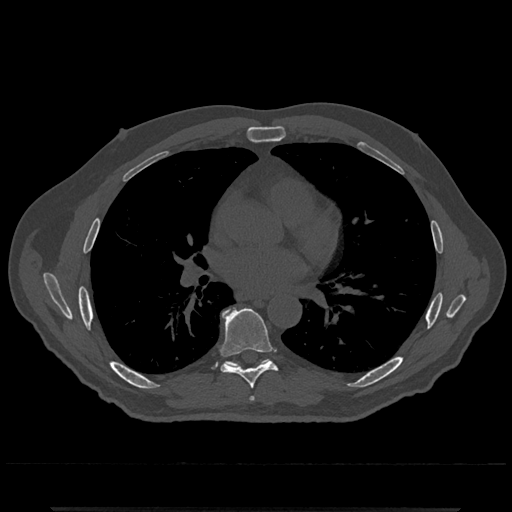
CT including the spine, one axial slice; position 713 of 797 along the scan axis; reconstruction kernel Br40s/3; 120 kVp; bone window (W 1800 / L 400 HU); 512 × 512 image matrix, field of view 393 × 393 mm. Patient: male, 67 years. From the clinical record (not read from this slice): primary cancer: prostate.
Structures marked on this image (semi-automatic segmentation, software-assisted and operator-edited):
- T6 vertebra: bounding box <250,397,254,400> (left, top, right, bottom; pixels)
- T7 vertebra: <220,308,277,389>
- T8 vertebra: <224,359,270,367>